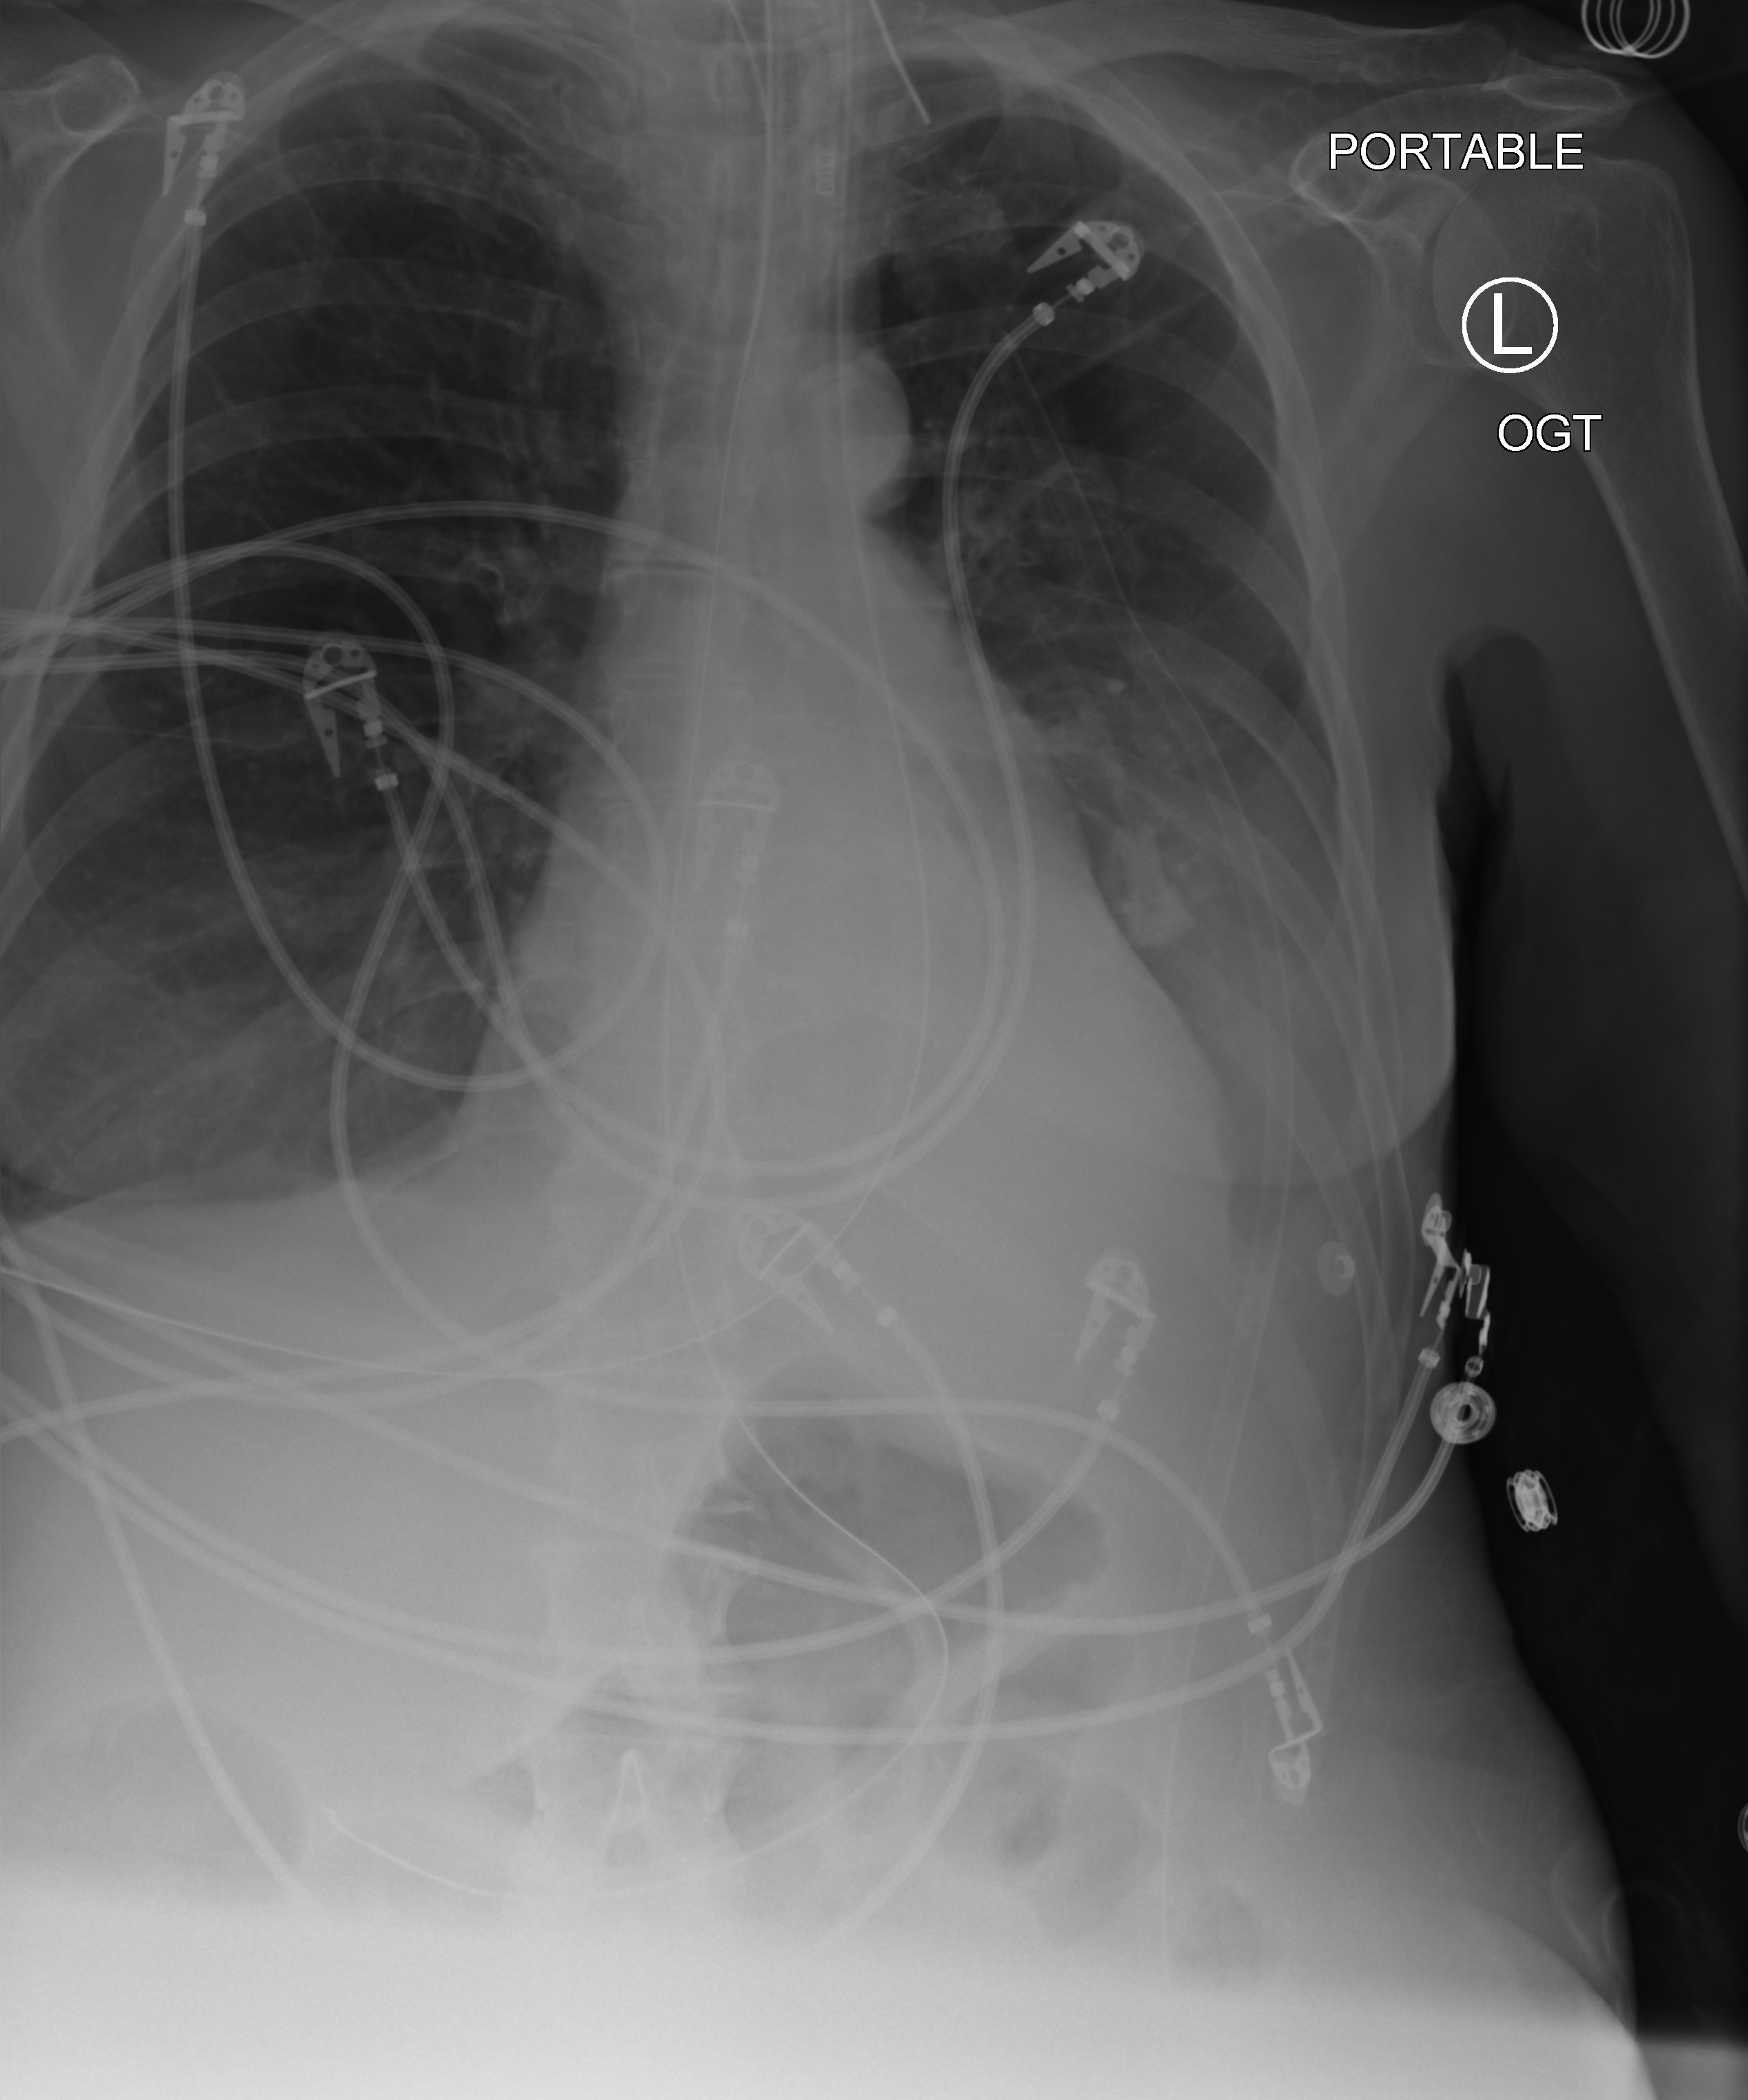
Portable chest radiograph; anteroposterior (AP) projection. Patient hospitalised with COVID-19; female, aged 60–74 years.
Admission-level facts for this patient (not findings on this image; timing relative to this image not recorded): length of hospital stay: 38 days.